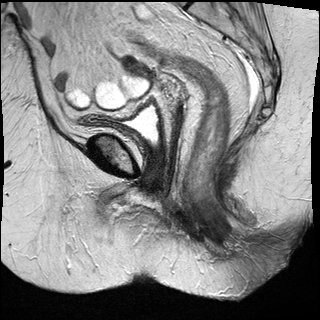
Pelvic MRI for cervical cancer, one sagittal slice. Slice 16 of 27 in the series (ordered by position). T2-weighted. 1.5 T. TE 89 ms, TR 2740 ms. 4 mm slice thickness. 320 × 320 image matrix. Female patient, age 67 years.
Structures marked on this image (outlined manually by an expert reader):
- uterus and cervix: bounding box [x1, y1, x2, y2] px = [123, 54, 154, 81]